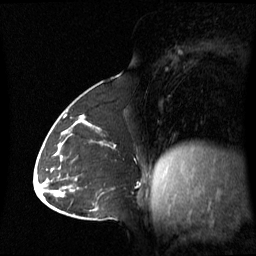
Breast MRI (dynamic contrast-enhanced), one sagittal slice. Slice 29 of 60 in the series (ordered by position). Dynamic contrast-enhanced series, image 2 of 3 at this slice position (ordered by acquisition). 1.5 T. TE 4.2 ms, TR 8.4 ms. 256 × 256 image matrix, field of view 270 × 270 mm. Patient: female, 43 years. Case-level facts recorded for this patient, not image findings: setting: breast cancer imaged before/during neoadjuvant chemotherapy; receptor status: triple-negative.
Structures marked on this image (semi-automatically segmented with operator editing):
- analysis volume of interest (the breast-tissue region the enhancement analysis was run in; not a lesion): box from (x=62, y=124) to (x=116, y=180) px
- tumour enhancement mask (voxels above the 70 % enhancement threshold inside the analysis volume of interest): (x=62, y=130)–(x=66, y=135)